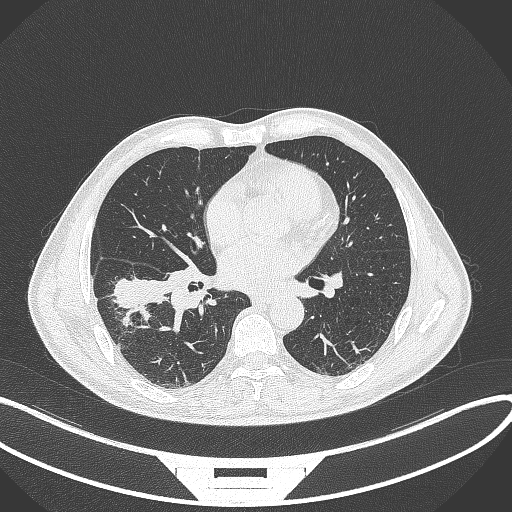
Chest CT, one axial slice. Position 168 of 364 along the scan axis. Lung window (W 1500 / L -600 HU). 1 mm slice thickness. 512 × 512 image matrix, field of view 400 × 400 mm. Male patient, age 58 years. Case-level facts recorded for this patient, not image findings: clinical TNM (as recorded): T3 N0 M0; histopathological grade: G2.
Outlined on this slice (bounding box drawn by a radiologist):
- lung tumour (recorded histology: squamous cell carcinoma): bounding box <110,273,171,314> (left, top, right, bottom; pixels)